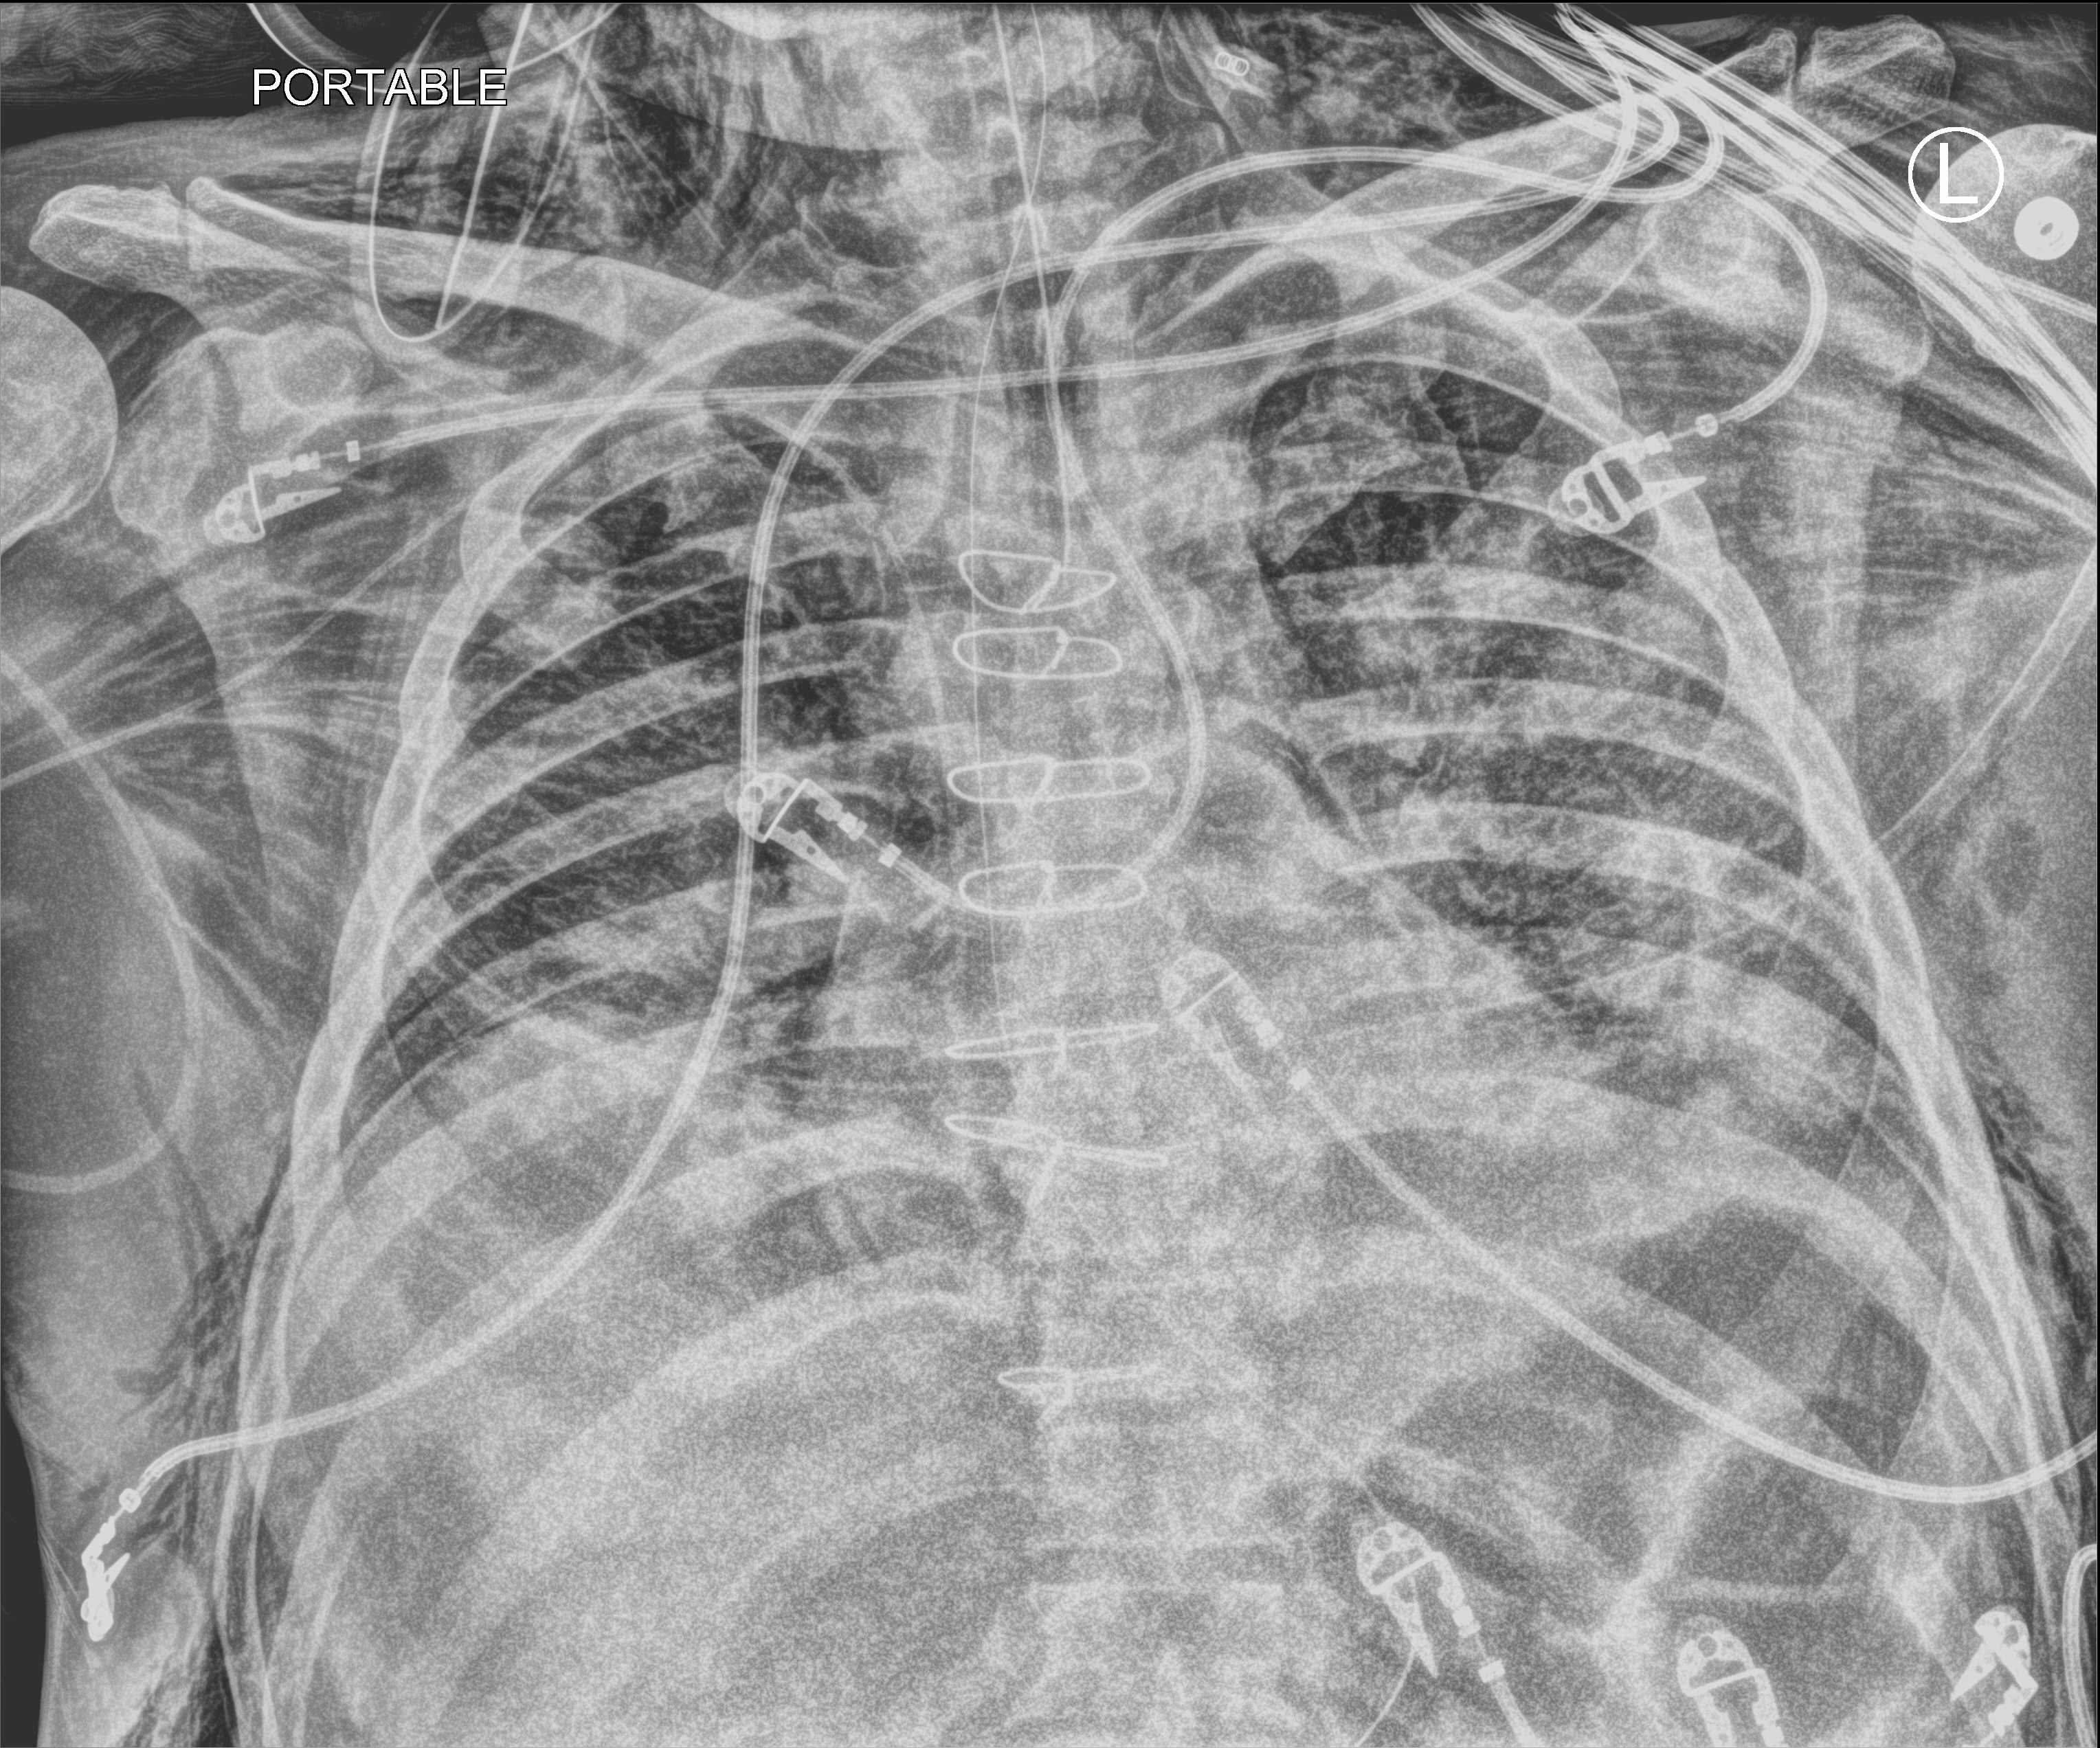
Portable chest radiograph. Patient hospitalised with COVID-19; male, aged 60–74 years.
Admission-level facts for this patient (not findings on this image; timing relative to this image not recorded):
- admitted to intensive care during this hospital stay: yes
- mechanically ventilated during this hospital stay: yes